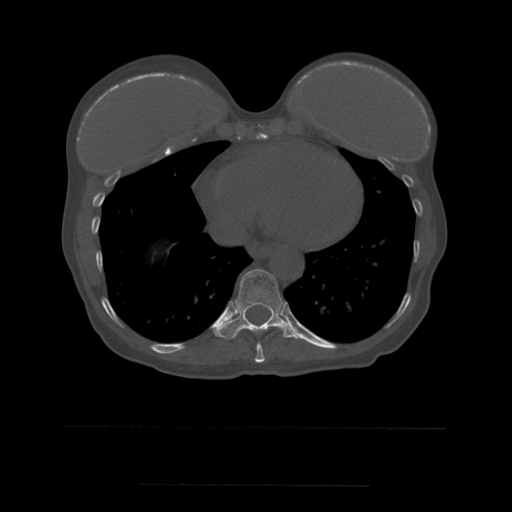
CT including the spine, one axial slice; position 307 of 544 along the scan axis; bone window (W 1800 / L 400 HU); 1.25 mm slice thickness; 512 × 512 image matrix. Patient age 58 years. Case-level facts recorded for this patient, not image findings: primary cancer: lung.
Outlined on this slice (semi-automatically segmented with operator editing):
- T10 vertebra: bounding box [x1, y1, x2, y2] px = [215, 269, 297, 339]
- T9 vertebra: [255, 343, 265, 363]